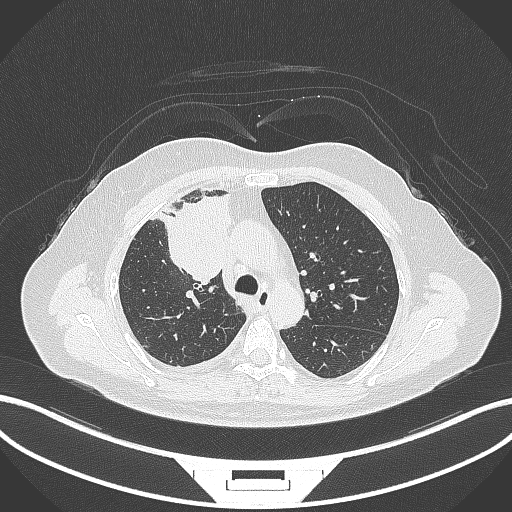
Chest CT, one axial slice. Reconstruction kernel B70f. 120 kVp. Lung window (W 1500 / L -600 HU). 512 × 512 image matrix. Patient: female, 52 years. Case-level facts recorded for this patient, not image findings: clinical TNM (as recorded): T3 N1 M1.
Structures marked on this image (rectangle marked by the reading radiologist):
- lung tumour (recorded histology: adenocarcinoma): bounding box <160,193,233,284> (left, top, right, bottom; pixels)